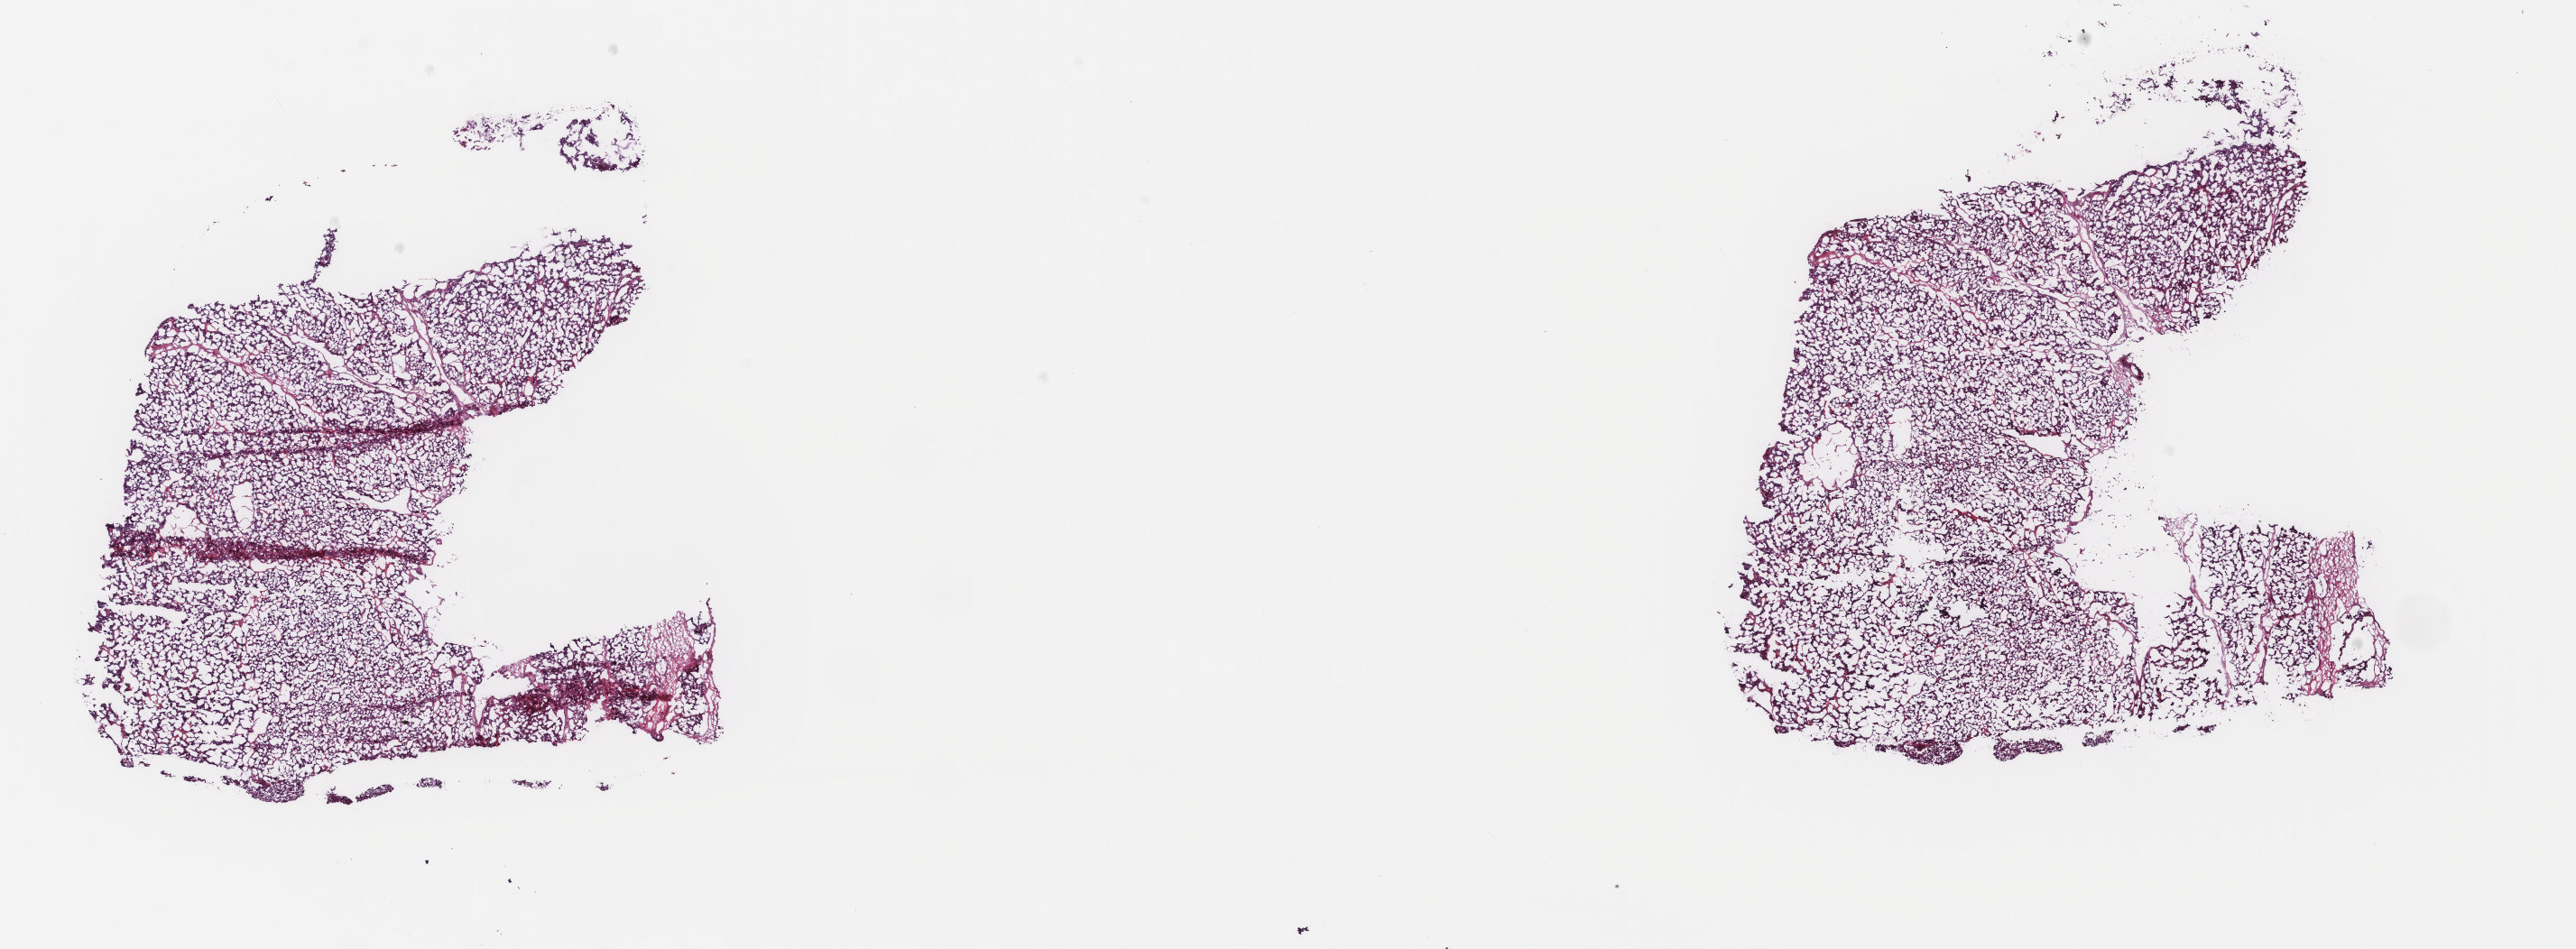
Whole-slide histology image, Hematoxylin and eosin (H&E) stained — whole scanned area (about 22.7 x 8.4 mm, from a 40x scan) shown as a low-resolution overview; frozen section from the top of the tissue portion; liver, primary tumour sample. Male, age 67 years at initial diagnosis. Histologic grade: G3 (poorly differentiated). Slide review estimates, as recorded: tumour cells 100%, tumour nuclei 96%, normal cells 0%, stromal cells 0%, necrosis 0%. Inflammatory infiltration, as recorded: lymphocyte infiltration 0%, monocyte infiltration 0%, neutrophil infiltration 0%.
- AJCC pathologic stage: IIIB (7th edition)
- diagnosis: Hepatocellular carcinoma, NOS